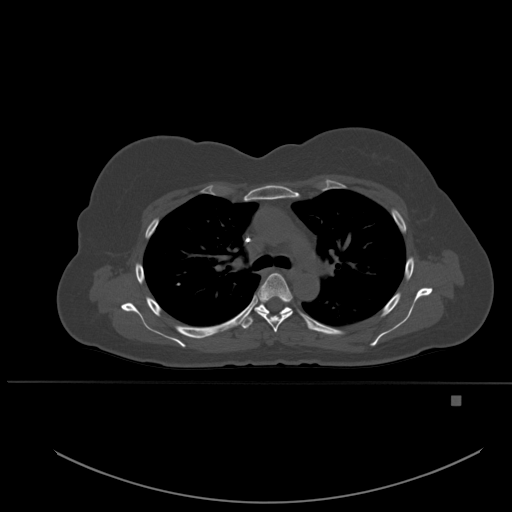
CT including the spine, one axial slice; bone window (W 1800 / L 400 HU); 512 × 512 image matrix, field of view 443 × 443 mm. Female patient, age 49 years. From the clinical record (not read from this slice): primary cancer: breast.
Annotated regions visible in this slice (semi-automatic segmentation, software-assisted and operator-edited):
- T4 vertebra: bounding box <255,273,293,333> (left, top, right, bottom; pixels)
- T5 vertebra: <241,303,293,329>